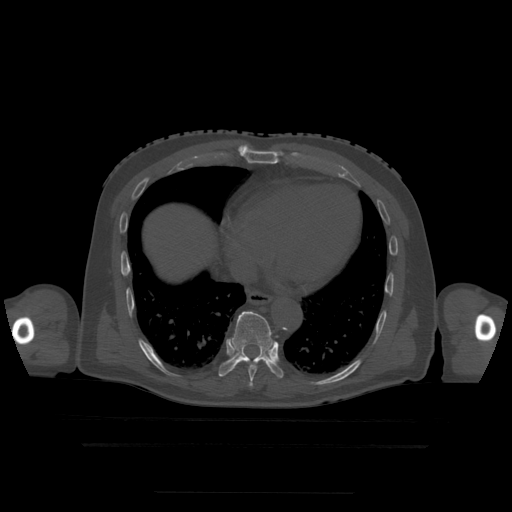
CT including the spine, one axial slice. Slice 268 of 522 in the series (ordered by position). Bone window (W 1800 / L 400 HU). 1.25 mm slice thickness. 512 × 512 image matrix, field of view 436 × 436 mm. Patient age 68 years. From the clinical record (not read from this slice): primary cancer: urothelial.
Annotated regions visible in this slice (semi-automatically segmented with operator editing):
- T7 vertebra: bounding box (x1, y1, x2, y2) in pixels: (250, 381, 253, 387)
- T8 vertebra: (247, 362, 257, 381)
- T9 vertebra: (219, 312, 284, 379)